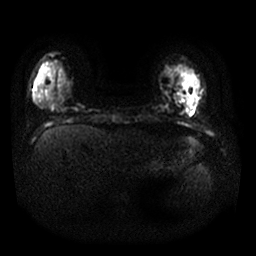
Breast MRI, one axial slice; position 1 of 25 along the scan axis; diffusion-weighted series; image 2 of 4 stored at this slice position (different b-values; order by instance number); 1.5 T; 256 × 256 image matrix, field of view 330 × 330 mm. Female patient.
Annotated regions visible in this slice (manually delineated by an expert):
- tumour on diffusion-weighted imaging: box from (x=187, y=102) to (x=191, y=105) px